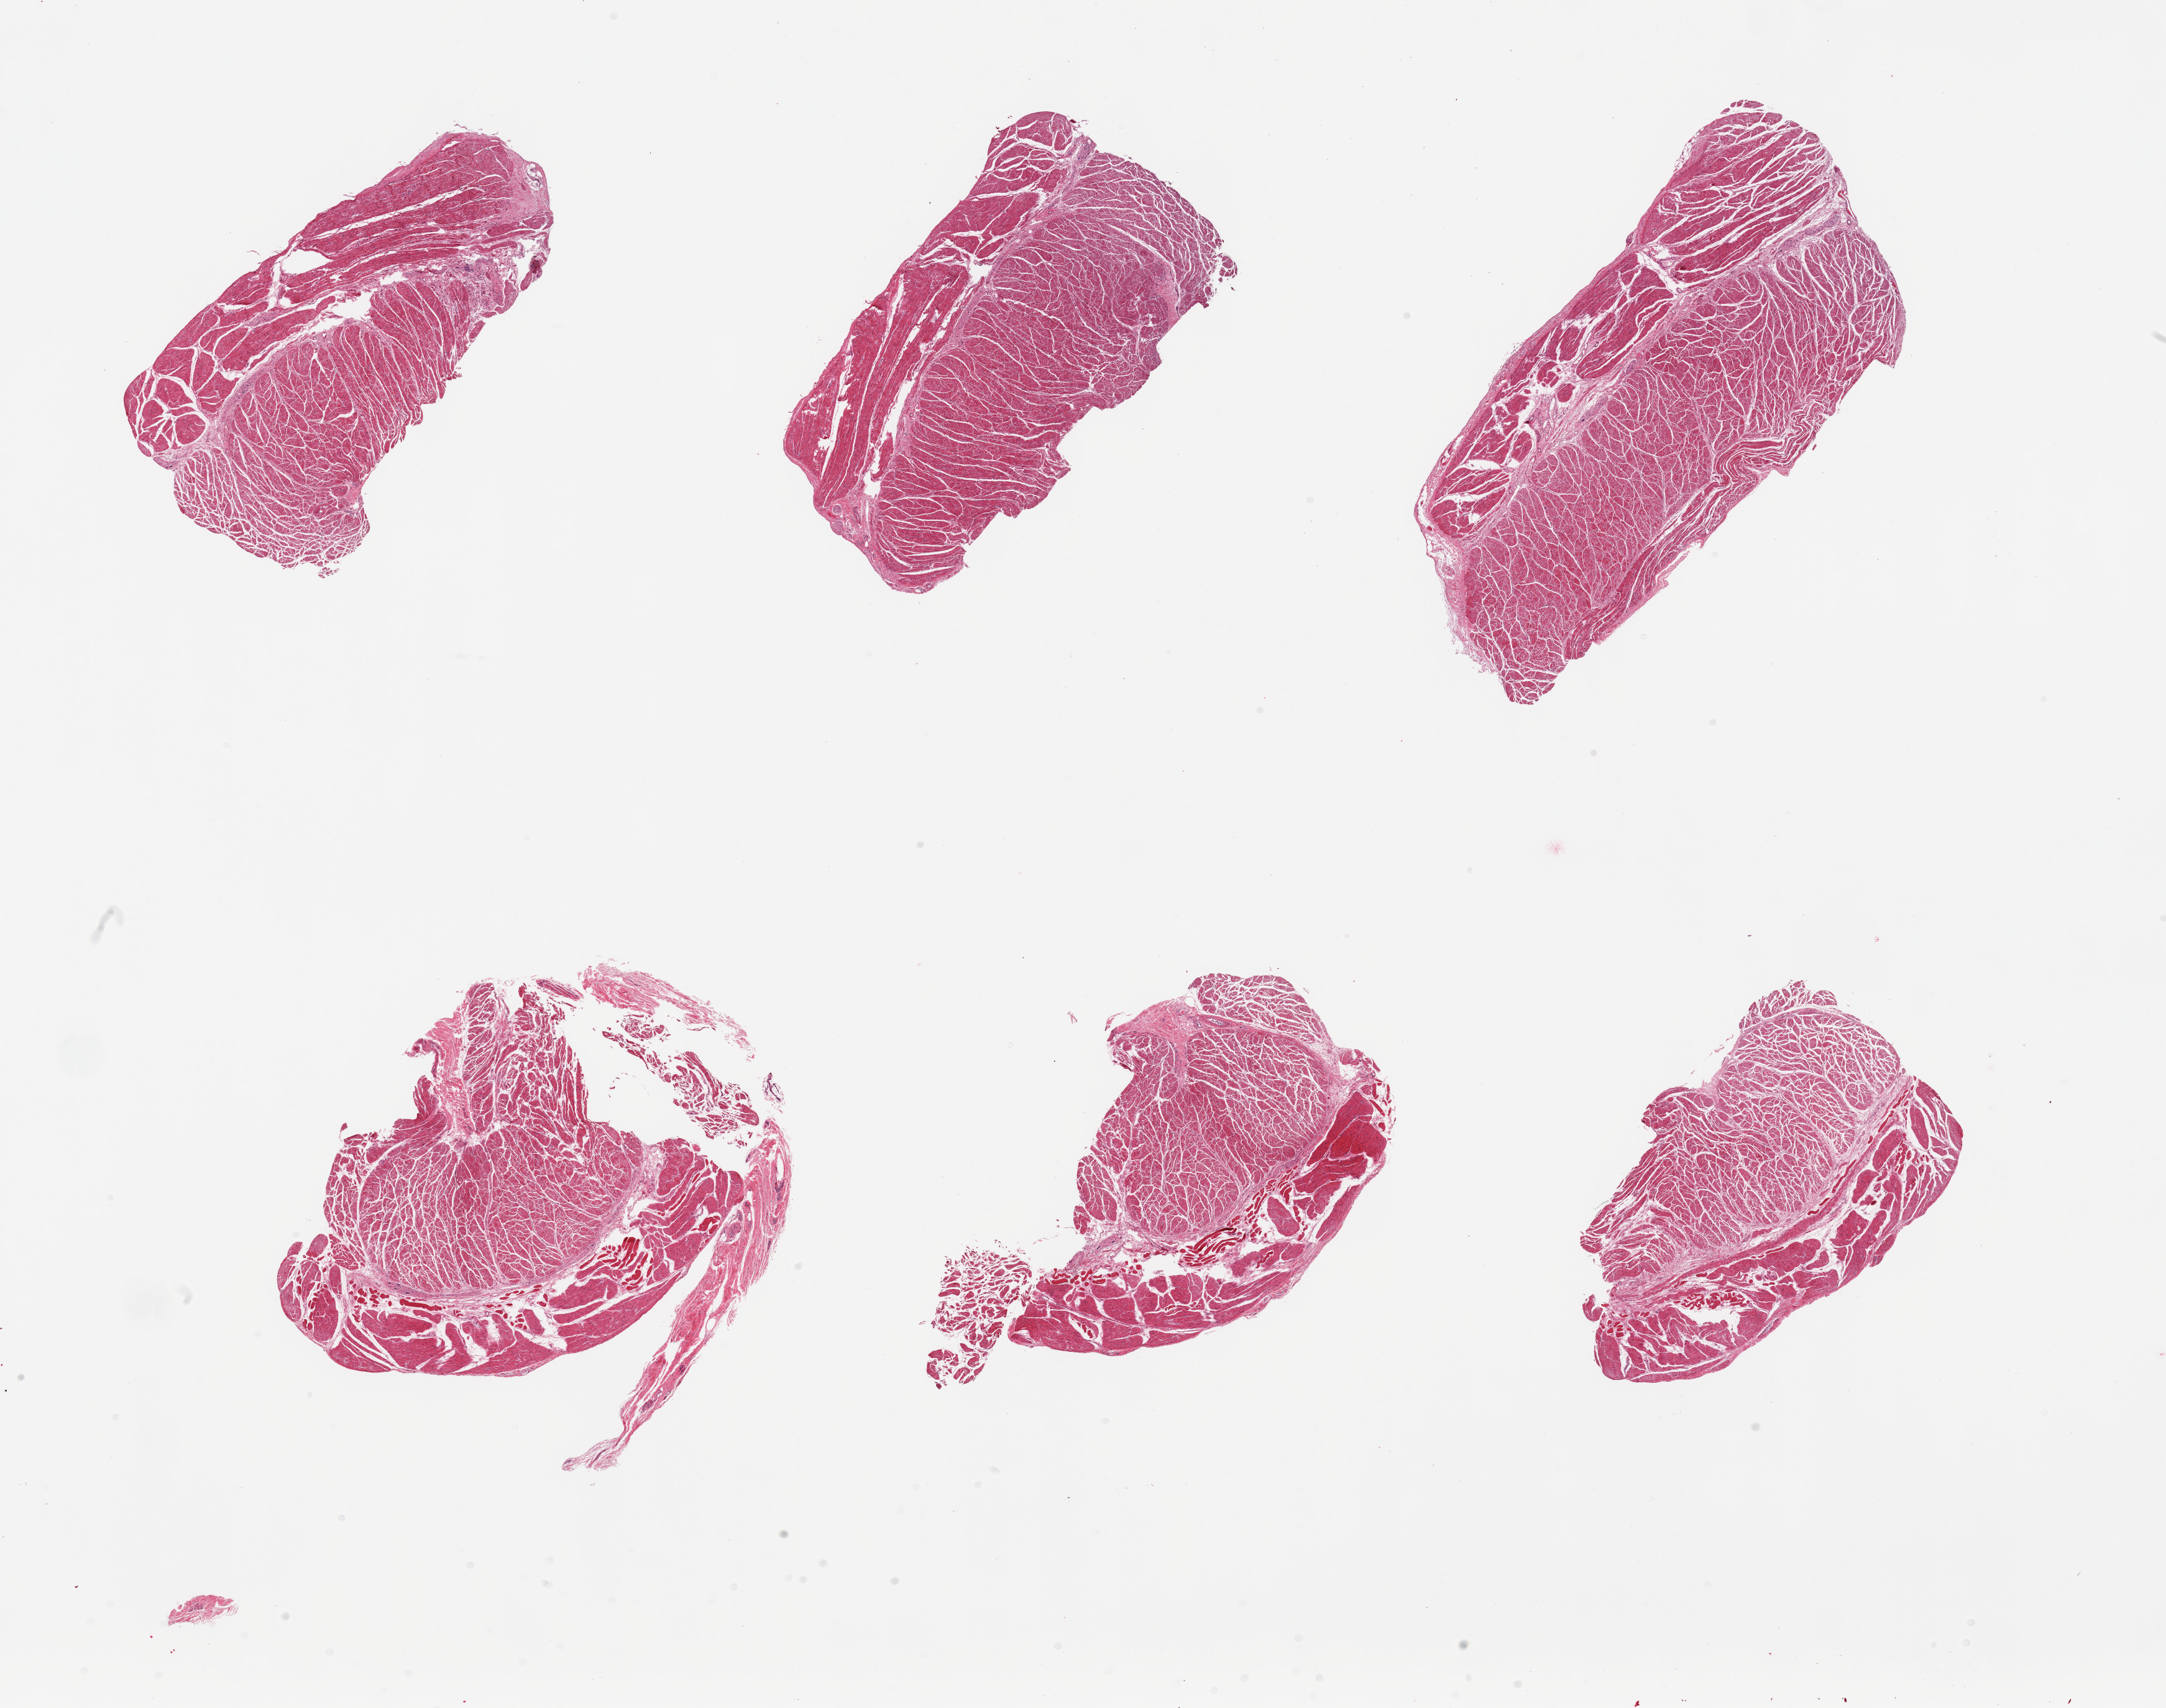
Whole-slide image, hematoxylin and eosin (H&E) stain — shown as a low-resolution overview of the whole scanned area (about 27.6 x 21.7 mm, acquisition: 20x scan). PAXgene-fixed paraffin-embedded (PFPE) section. Sampled site (target tissue): esophageal muscle. Donor tissue sample. Male donor.
* reviewer comment on this tissue sample: 6 pieces; well trimmed